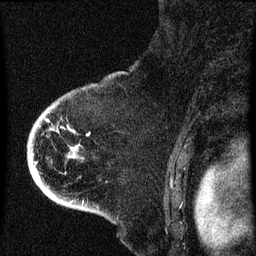
Breast MRI (dynamic contrast-enhanced), one sagittal slice. Position 51 of 60 along the scan axis. Dynamic contrast-enhanced series, image 2 of 4 at this slice position (ordered by acquisition). 1.5 T. TE 4.2 ms, TR 8 ms. 2 mm slice thickness. 256 × 256 image matrix. Female patient, age 71 years.
Outlined on this slice (semi-automatically segmented with operator editing):
- analysis volume of interest (the breast-tissue region the enhancement analysis was run in; not a lesion): box from (x=32, y=86) to (x=107, y=205) px
- tumour enhancement mask (voxels above the 70 % enhancement threshold inside the analysis volume of interest): (x=35, y=120)–(x=75, y=165)